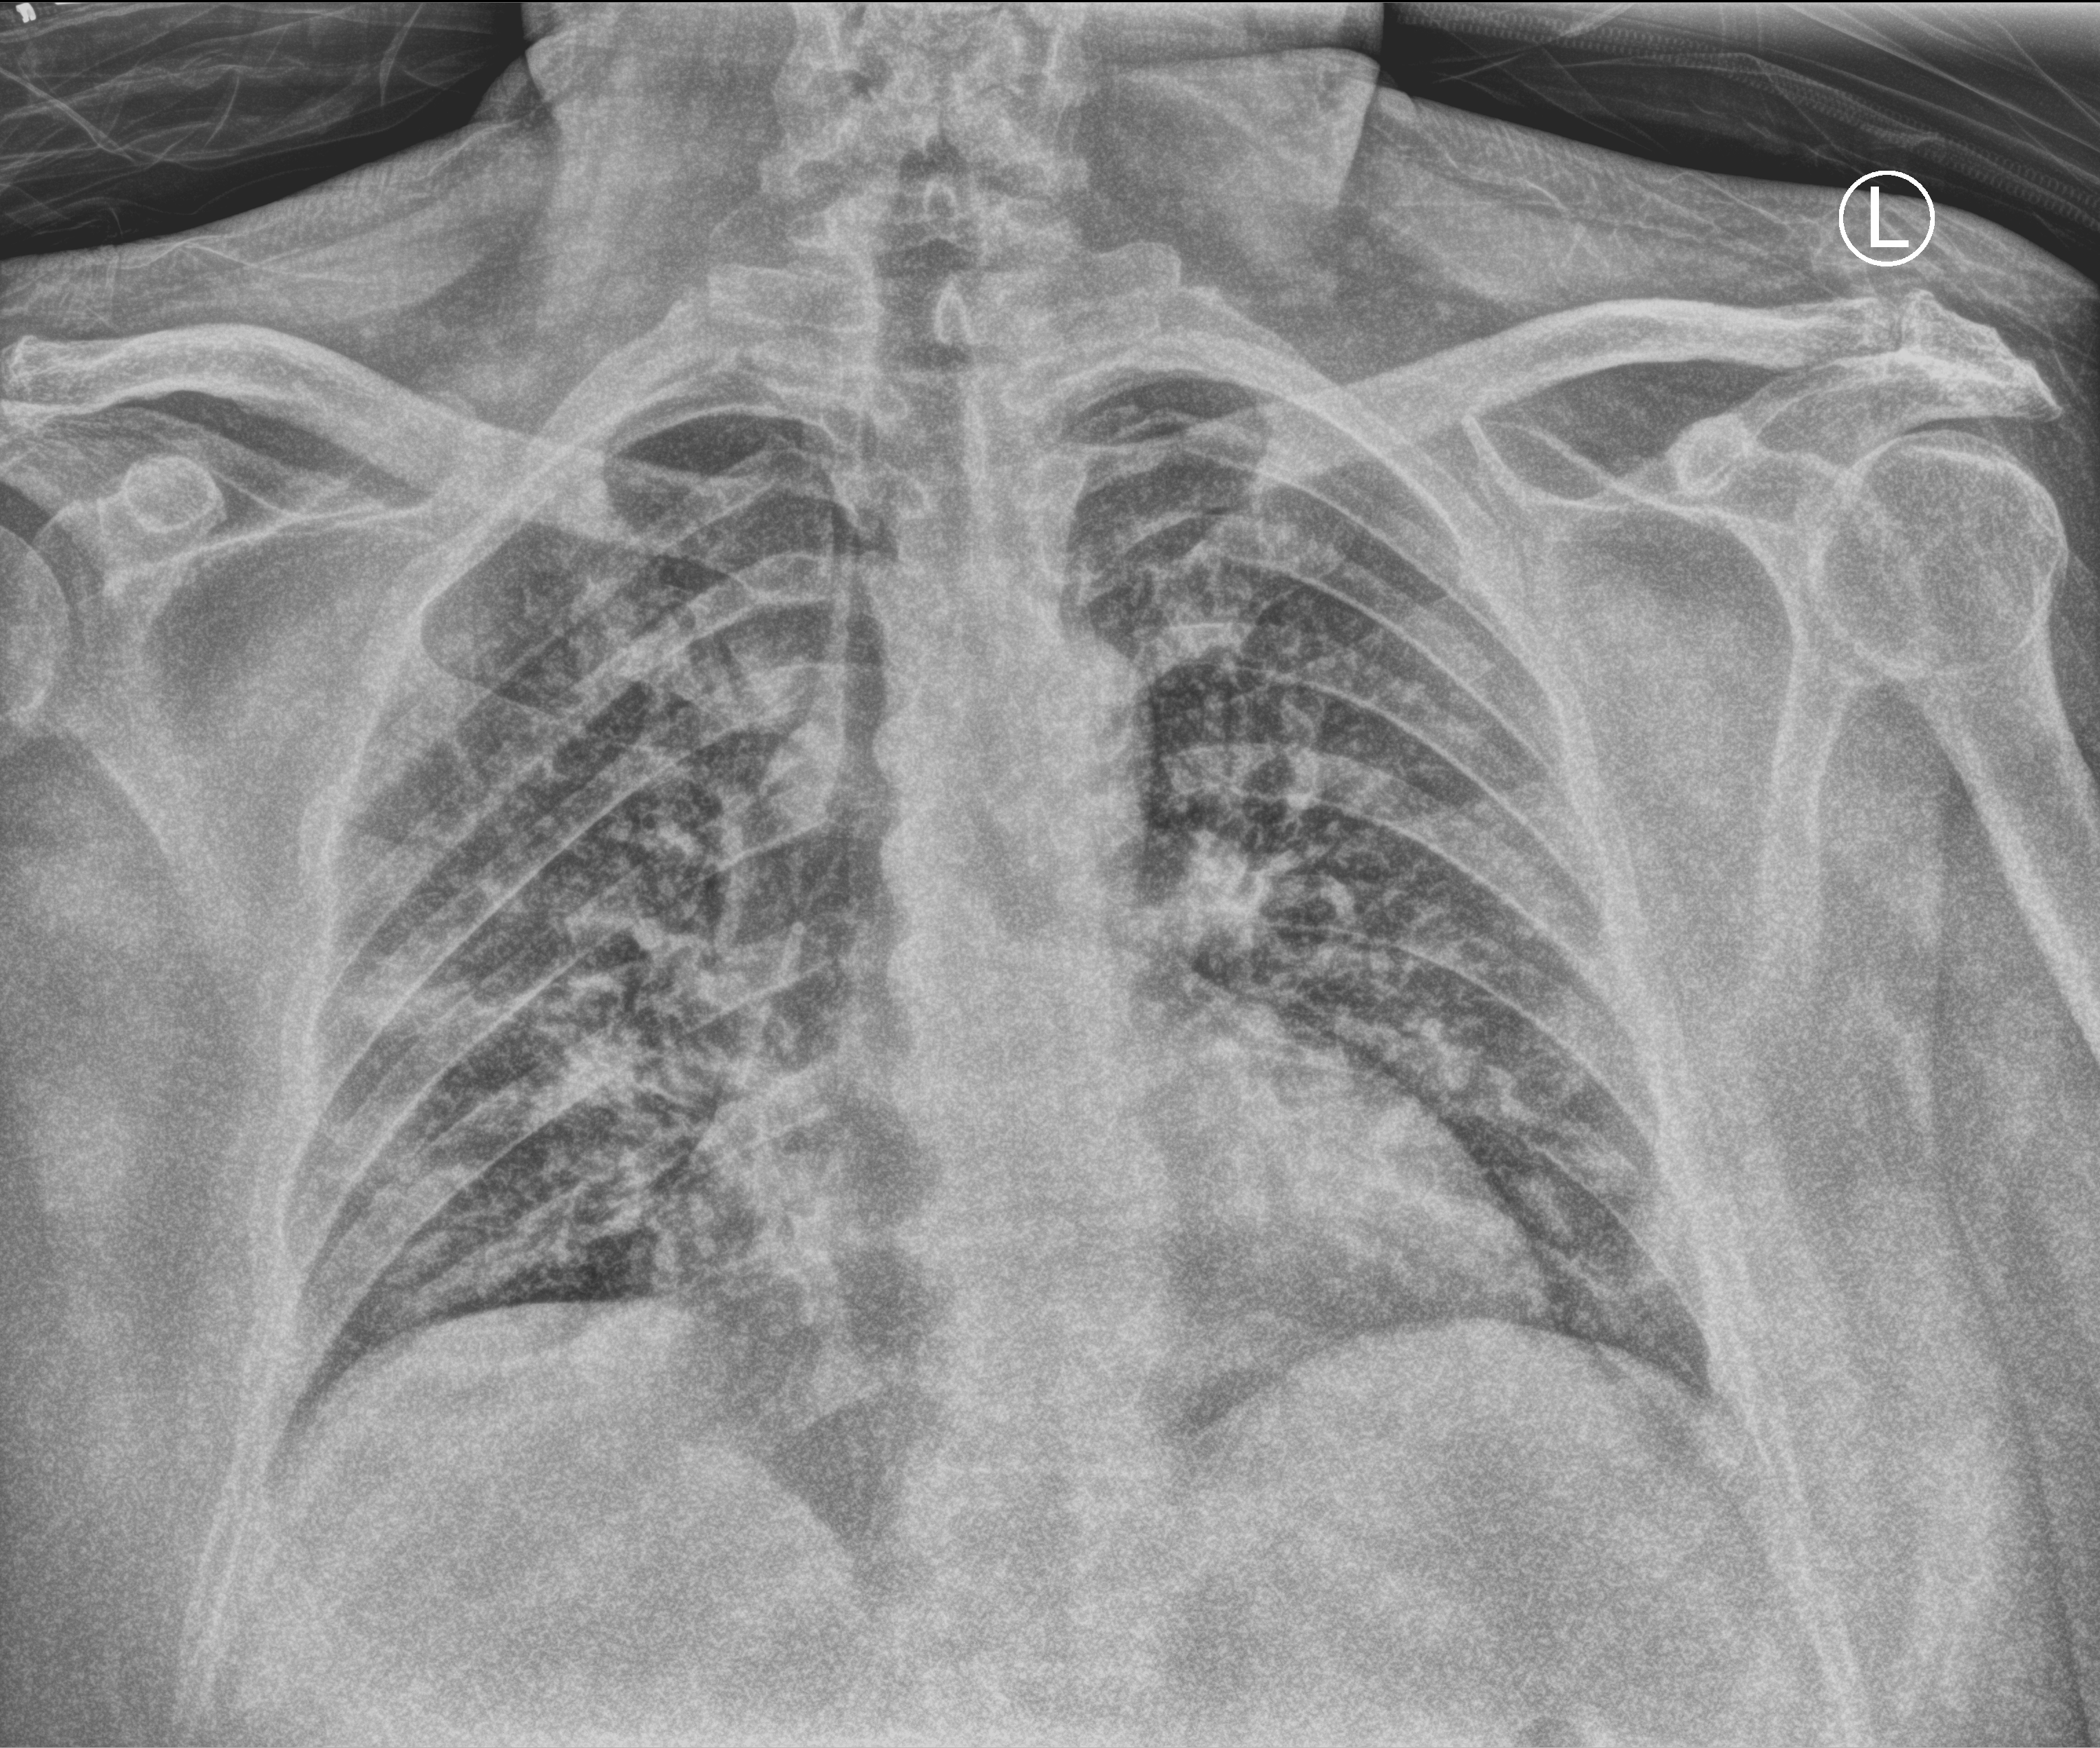
Portable chest radiograph, anteroposterior (AP) projection. Patient hospitalised with COVID-19; male, aged 18–59 years.
Admission-level facts for this patient (not findings on this image; timing relative to this image not recorded): admitted to intensive care during this hospital stay: no; mechanically ventilated during this hospital stay: no; other chronic lung disease (admission record): no.